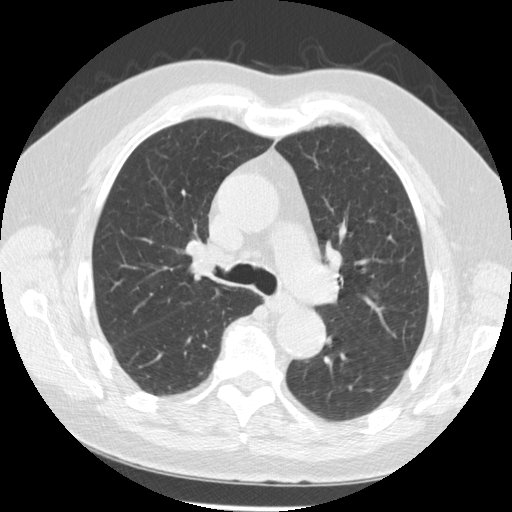
Low-dose screening chest CT, one axial slice; position 170 of 259 along the scan axis; reconstruction kernel STANDARD; lung window (W 1500 / L -600 HU); 512 × 512 image matrix, field of view 355 × 355 mm.
Structures marked on this image (manually delineated by an expert):
- lesion 2 (tumor, hilum of right lung): bounding box [x1, y1, x2, y2] px = [193, 243, 218, 275]